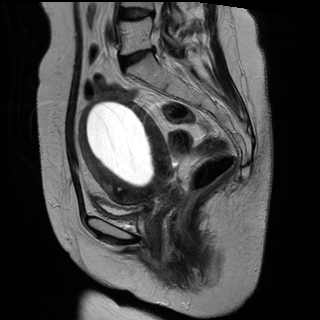
Pelvic MRI for cervical cancer, one sagittal slice; slice 17 of 29 in the series (ordered by position); T2-weighted; 1.5 T; TE 89 ms, TR 2930 ms; 4 mm slice thickness; 320 × 320 image matrix, field of view 260 × 260 mm. Female patient, age 49 years.
Outlined on this slice (manually delineated by an expert):
- uterus and cervix: bounding box <78,92,182,212> (left, top, right, bottom; pixels)